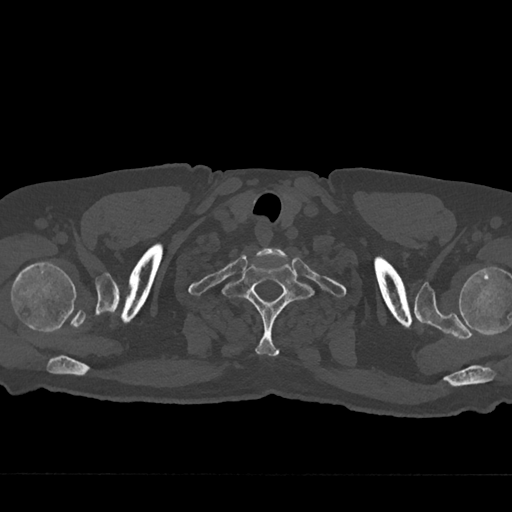
CT including the spine, one axial slice. Position 660 of 797 along the scan axis. Reconstruction kernel Br40s/3. 120 kVp. Bone window (W 1800 / L 400 HU). 0.5 mm slice thickness. 512 × 512 image matrix, field of view 377 × 377 mm. Patient: male, 75 years. Case-level facts recorded for this patient, not image findings: primary cancer: renal; vertebrae with lytic lesions (as recorded): T4.
Annotated regions visible in this slice (semi-automatic segmentation, software-assisted and operator-edited):
- T1 vertebra: box from (x=221, y=261) to (x=315, y=356) px
- T2 vertebra: (x=280, y=293)–(x=283, y=296)